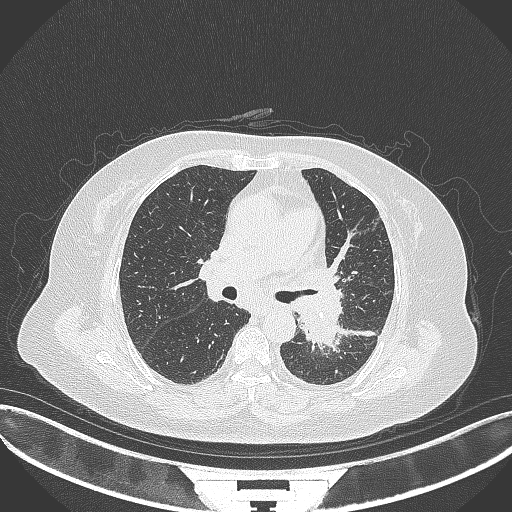
Chest CT, one axial slice; slice 203 of 322 in the series (ordered by position); 120 kVp; lung window (W 1500 / L -600 HU); 1 mm slice thickness; 512 × 512 image matrix, field of view 400 × 400 mm. Female patient, age 69 years. From the clinical record (not read from this slice): clinical TNM (as recorded): T2b N3 M1.
Outlined on this slice (rectangle marked by the reading radiologist):
- lung tumour (recorded histology: adenocarcinoma): box from (x=287, y=285) to (x=344, y=351) px